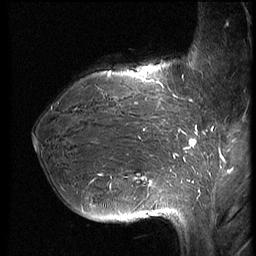
Breast MRI (dynamic contrast-enhanced), one sagittal slice. Position 23 of 66 along the scan axis. Dynamic contrast-enhanced series, image 2 of 3 at this slice position (ordered by acquisition). 1.5 T. TE 4.2 ms, TR 8.9 ms. 2.5 mm slice thickness. 256 × 256 image matrix, field of view 200 × 200 mm. Patient: female, 39 years. From the clinical record (not read from this slice): setting: breast cancer imaged before/during neoadjuvant chemotherapy; receptor status: HER2-positive.
Structures marked on this image (semi-automatic segmentation, software-assisted and operator-edited):
- analysis volume of interest (the breast-tissue region the enhancement analysis was run in; not a lesion): bounding box [x1, y1, x2, y2] px = [32, 75, 188, 218]
- tumour enhancement mask (voxels above the 140 % enhancement threshold inside the analysis volume of interest): [109, 75, 187, 192]